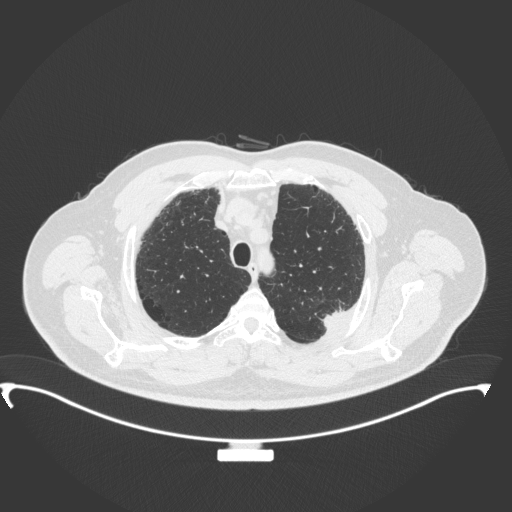
Chest CT, one axial slice; reconstruction kernel B31f; 120 kVp; lung window (W 1500 / L -600 HU); 1 mm slice thickness; 512 × 512 image matrix. Patient: male, 64 years. From the clinical record (not read from this slice): clinical TNM (as recorded): T1c N1 M1.
Outlined on this slice (bounding box drawn by a radiologist):
- lung tumour (recorded histology: adenocarcinoma): bounding box (x1, y1, x2, y2) in pixels: (318, 302, 352, 330)